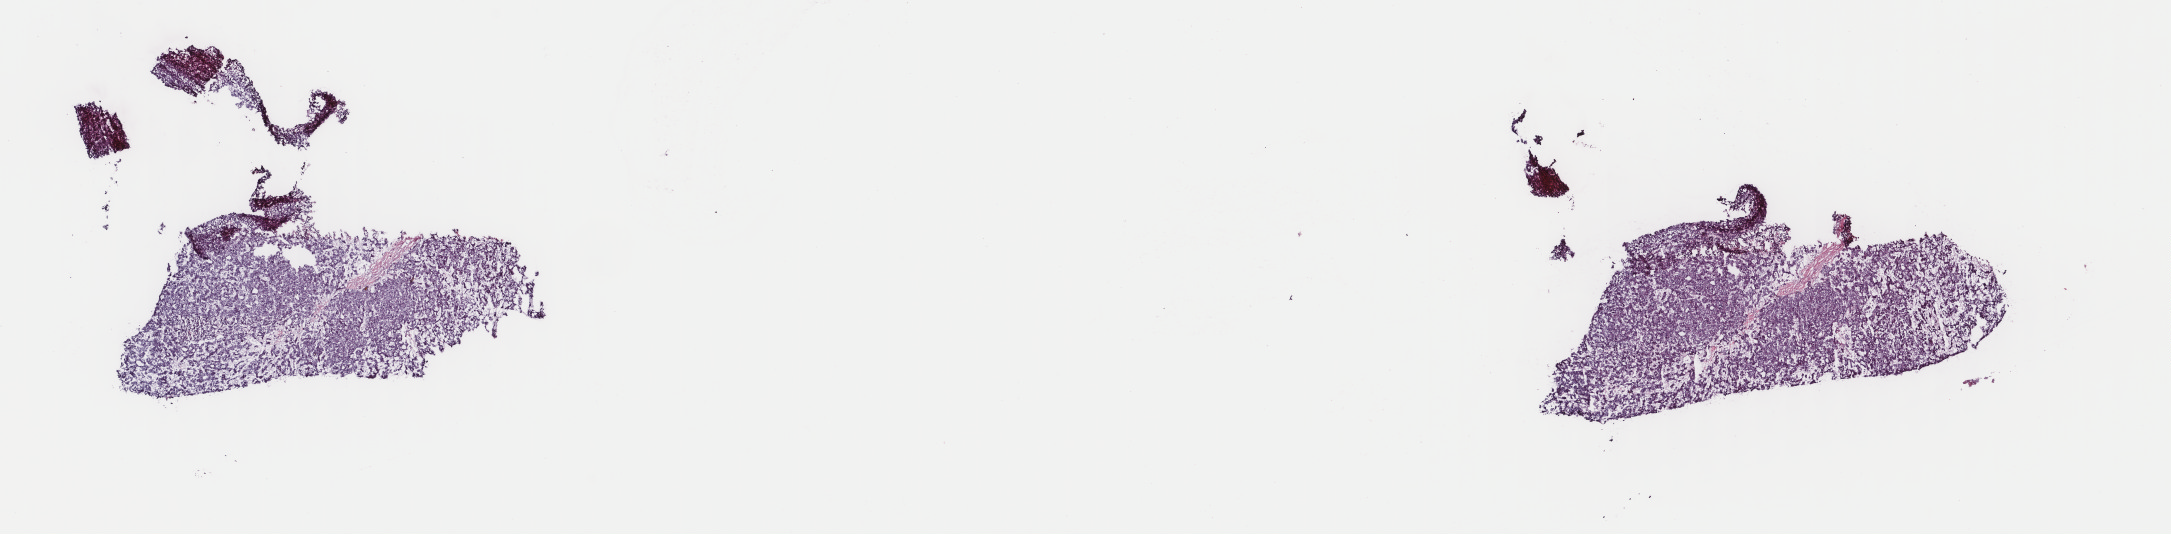
Digitized Hematoxylin and eosin (H&E) stained tissue section (whole slide) — low-resolution overview of the scanned area, about 17.2 x 4.2 mm (slide scanned at 40x); frozen section; primary tumour sample from the liver. Patient: male, age at initial diagnosis 69 years. Histologic grade: G1 (well differentiated). Pathologist review of this section (percent, as recorded): tumour cells 85%, tumour nuclei 85%, normal cells 0%, stromal cells 15%, necrosis 0%. Infiltration values recorded for this section: lymphocyte infiltration 2%, monocyte infiltration 1%, neutrophil infiltration 1%.
AJCC pathologic stage: I (7th edition). Diagnosis: Hepatocellular carcinoma, NOS.